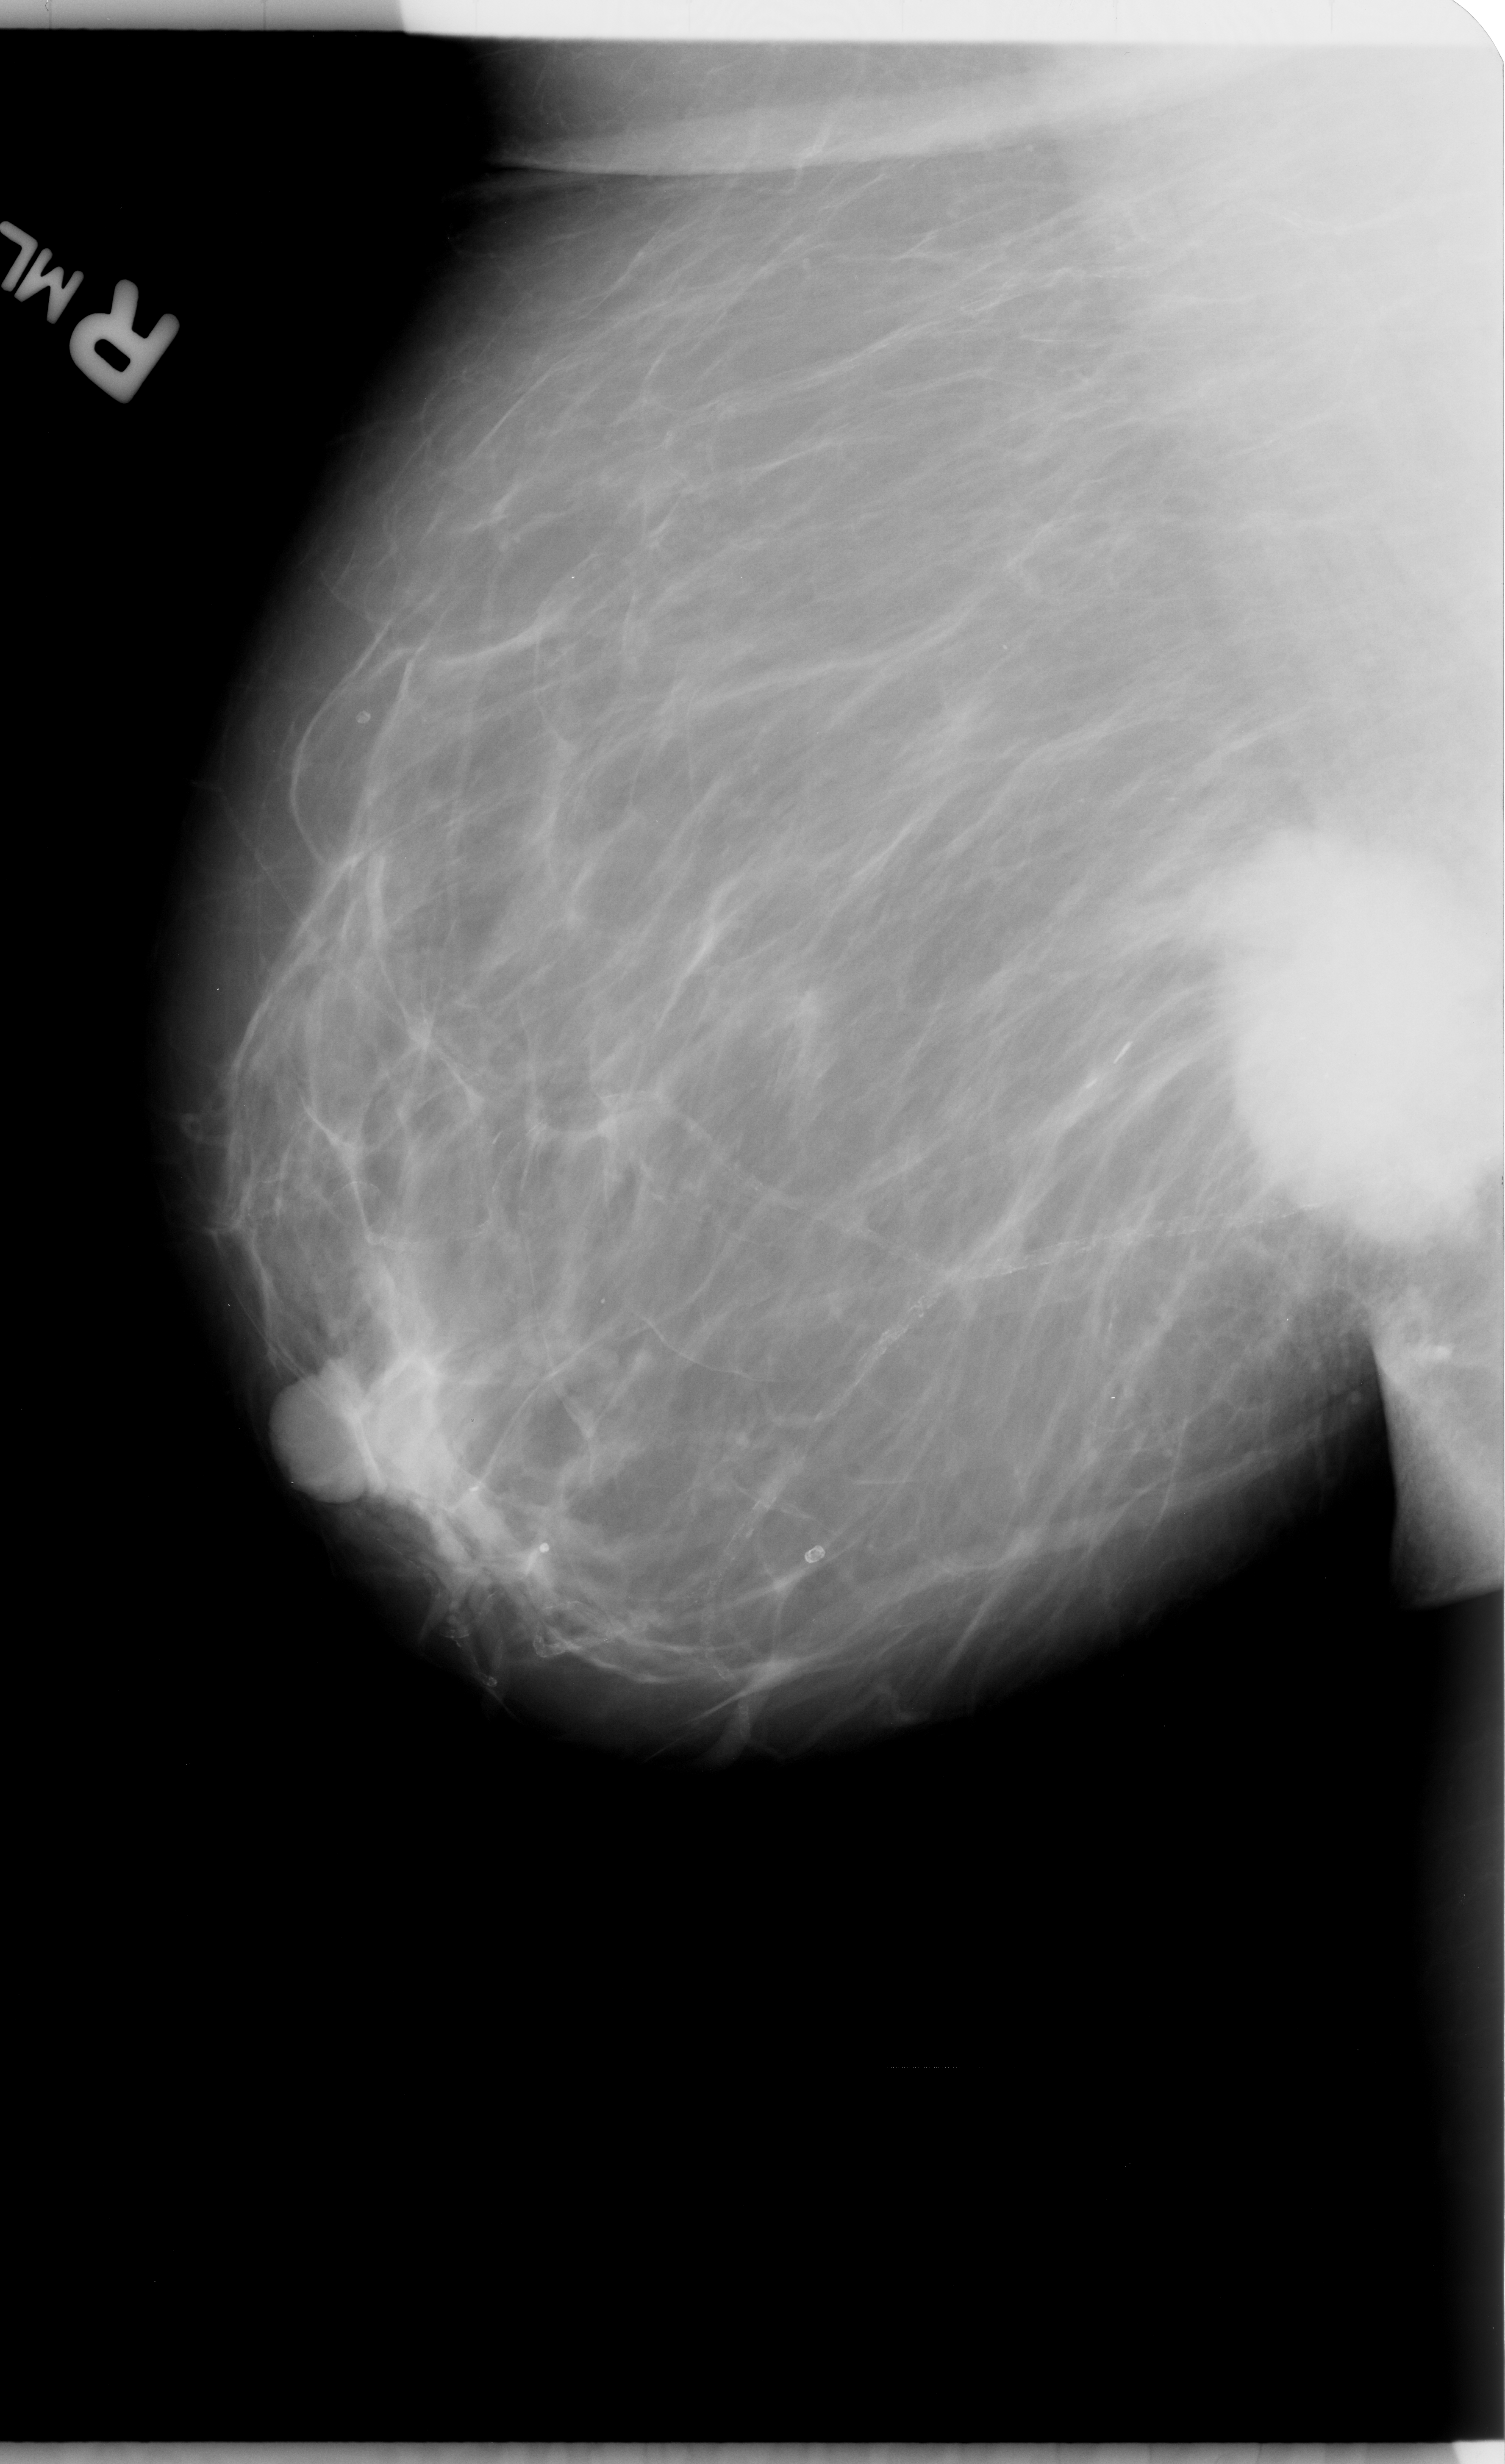
Scanned film-screen mammogram, right breast, mediolateral oblique (MLO) view, breast composition: almost entirely fatty (BI-RADS density category 1 of 4).
Marked abnormality: mass, shape irregular, margins spiculated; BI-RADS assessment category 4; subtlety rating 5 on a 1 (subtle) to 5 (obvious) scale; pathology (as recorded): malignant.